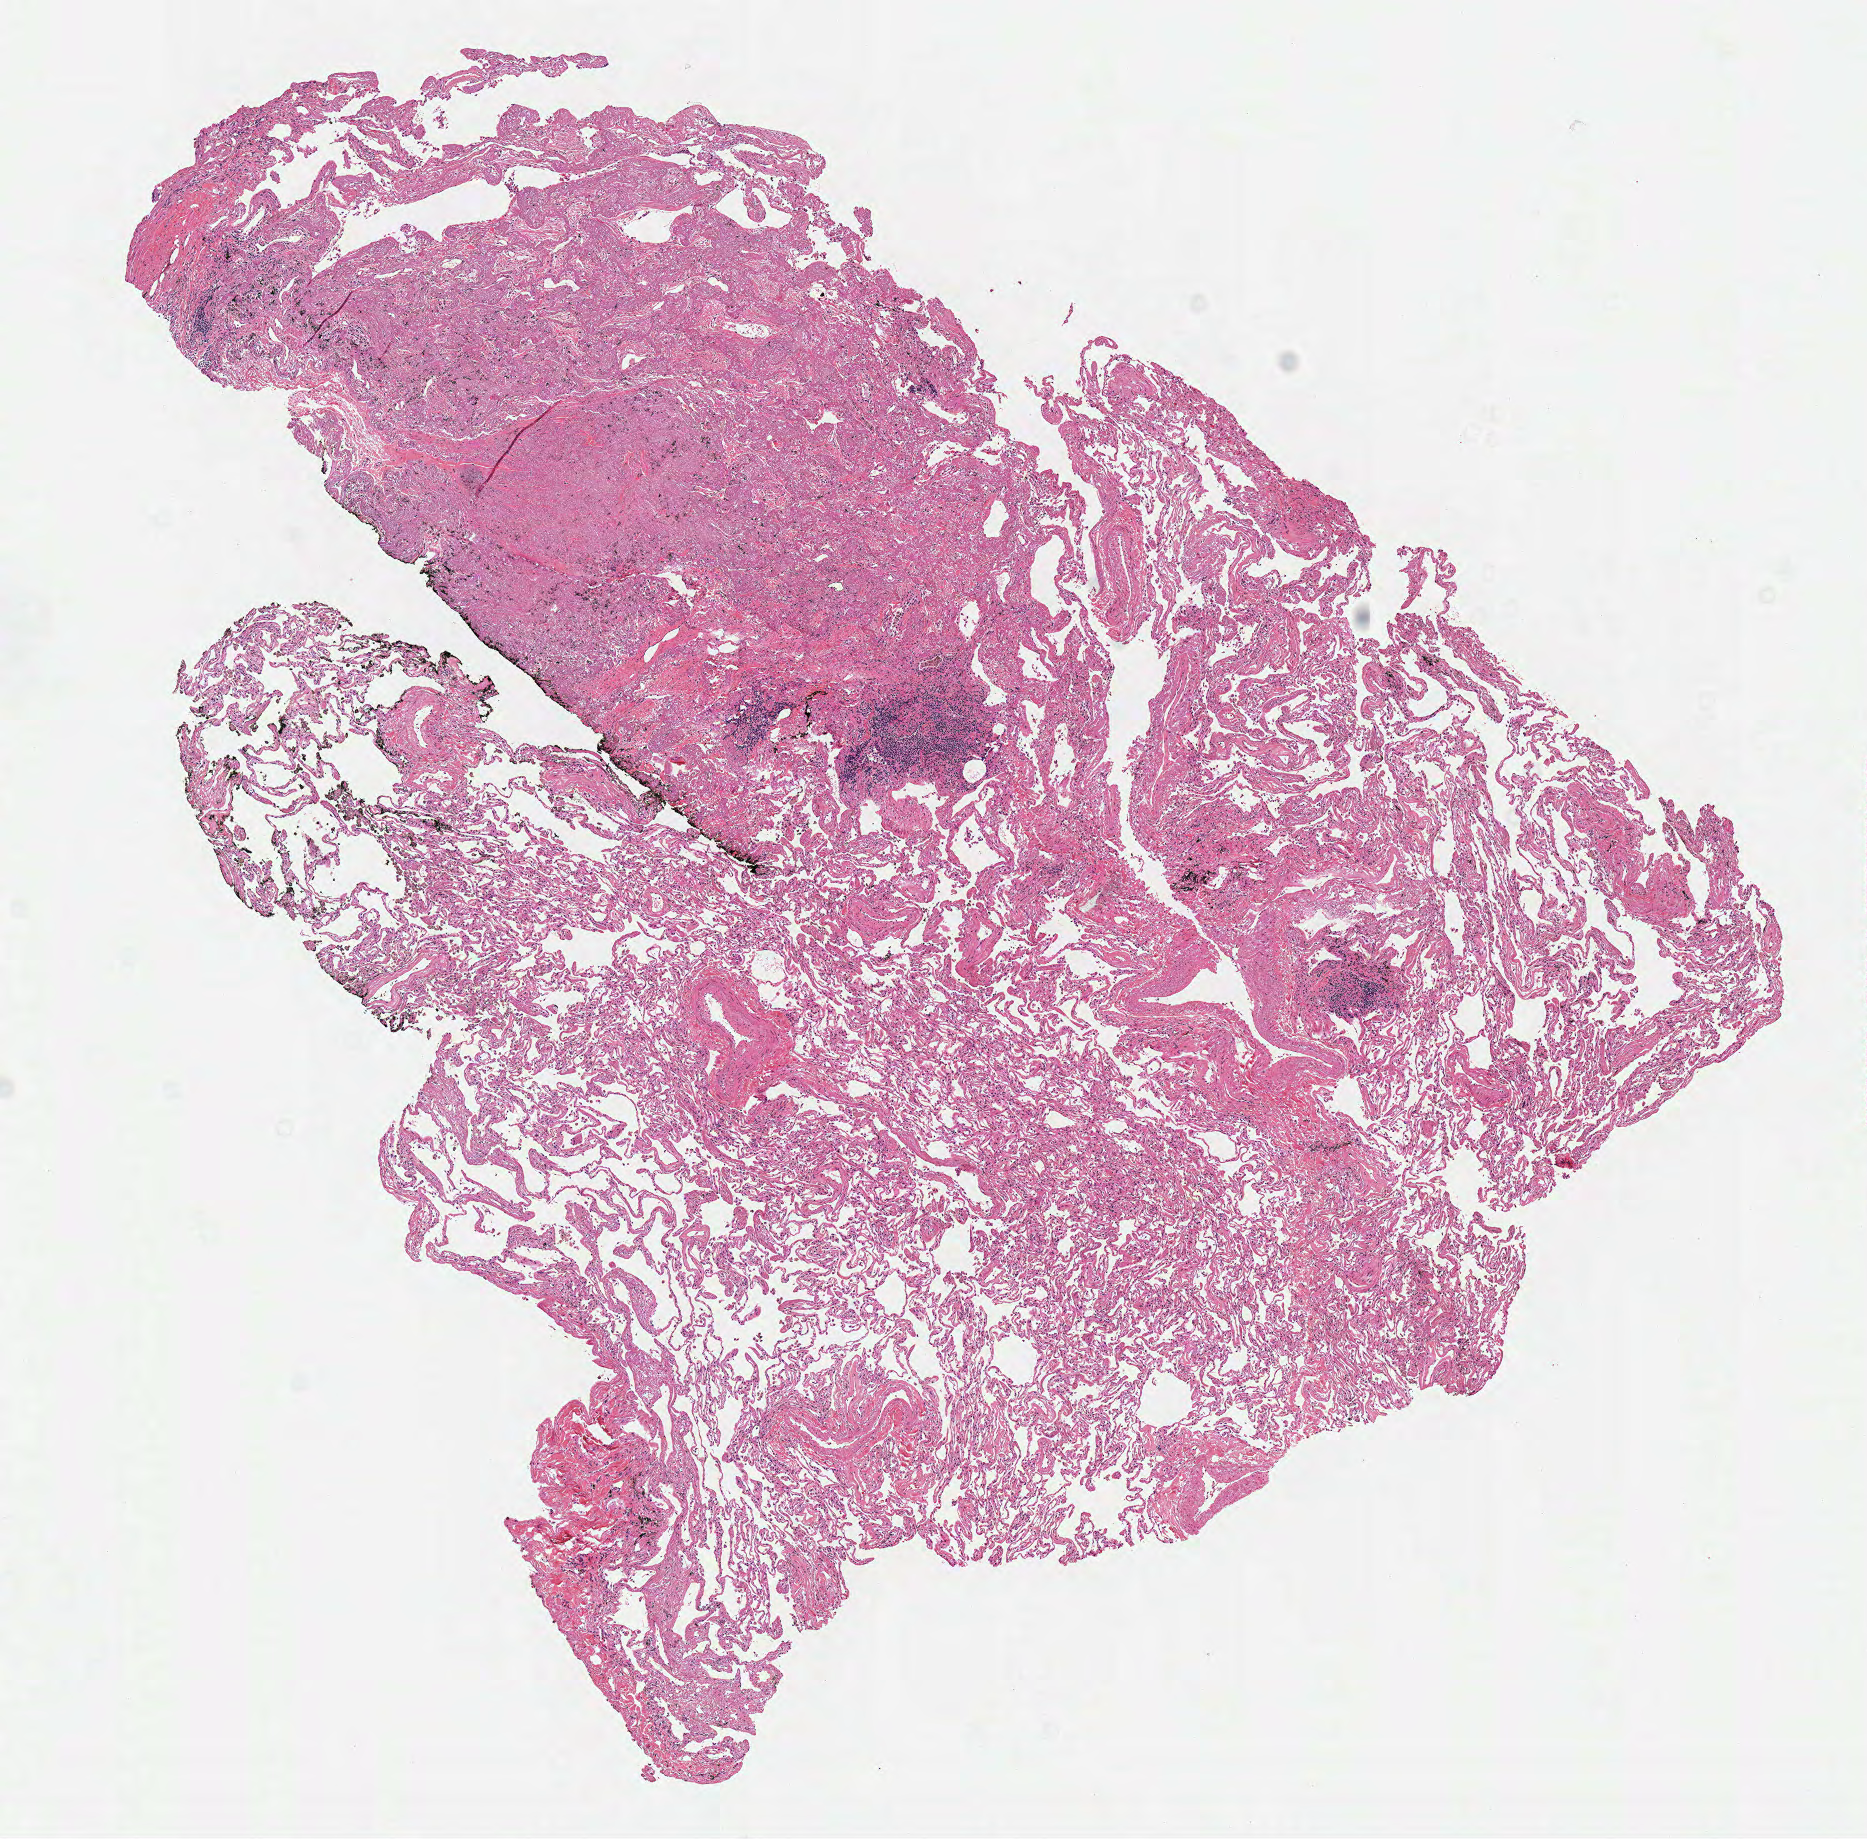
H&E-stained whole-slide image, shown as a low-resolution overview of the whole scanned area (about 7.3 x 7.2 mm); frozen section; lung, solid tissue normal (non-tumour tissue) sample. Patient: male, age at initial diagnosis 75 years.
This section: solid tissue normal (non-tumour) sample from the same patient. Patient diagnosis: Adenocarcinoma with mixed subtypes (upper lobe, lung).